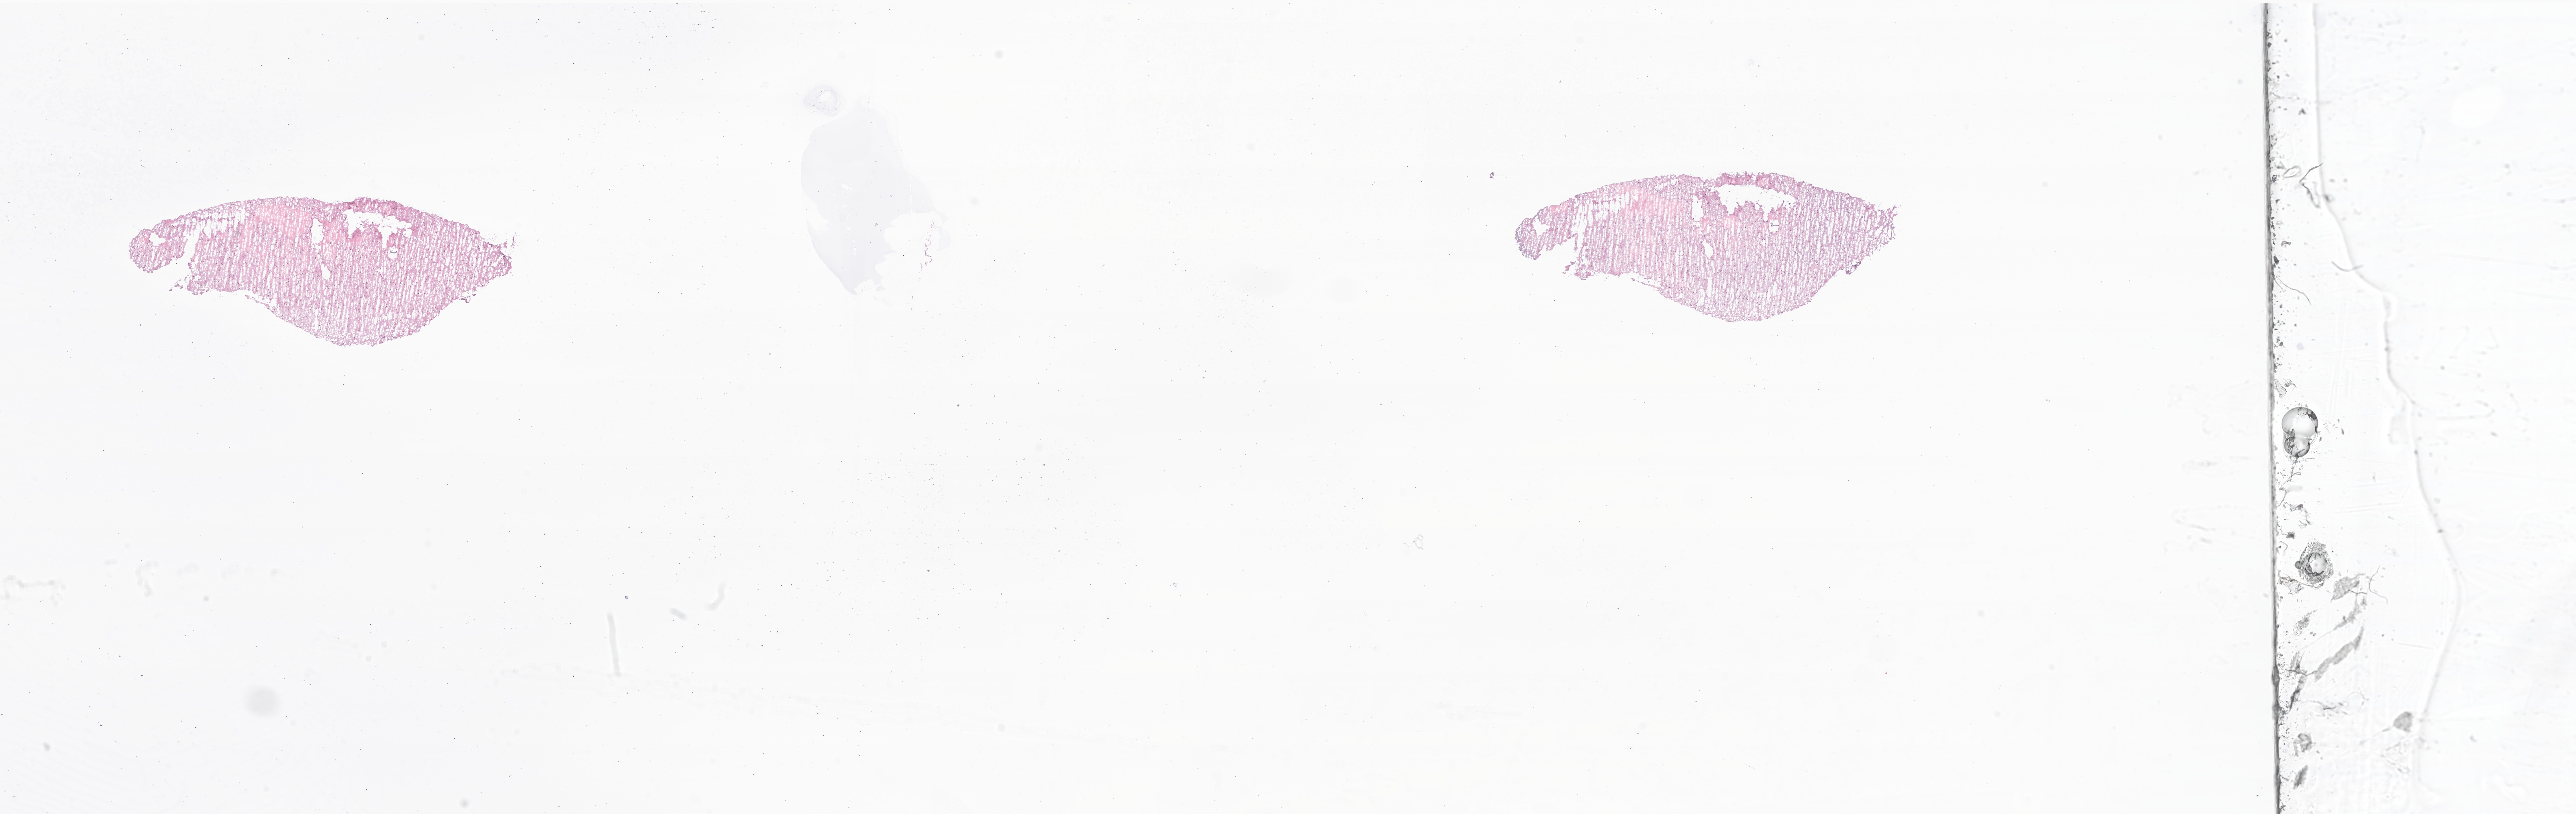
Whole-slide image, haematoxylin and eosin stain of tumor tissue from the brain, shown as a low-resolution overview of the whole scanned area (about 38.0 x 12.0 mm); frozen section (OCT-embedded). Patient: male, age 262 months (21 years 10 months).
Diagnosis: Astrocytoma, NOS.